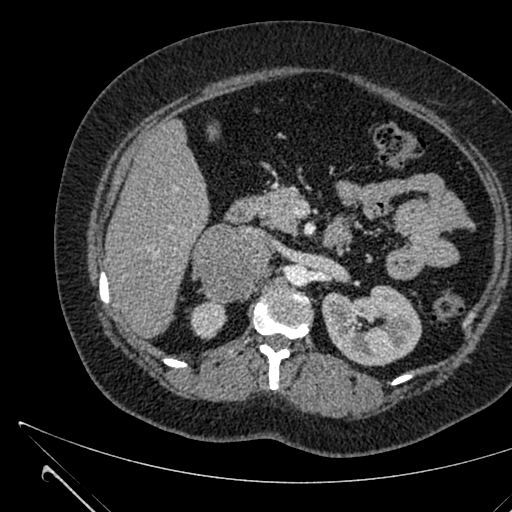
Contrast-enhanced abdominal CT, one axial slice; slice 383 of 731 in the series (ordered by position); soft-tissue window (W 400 / L 40 HU); 1 mm slice thickness; 512 × 512 image matrix, field of view 376 × 376 mm. Patient: female, 36 years. From the clinical record (not read from this slice): diagnosis: adrenocortical carcinoma; tumour side: right adrenal; tumour size at pathology: 10 cm.
Structures marked on this image (semi-automatic segmentation, software-assisted and operator-edited):
- mass: bounding box [x1, y1, x2, y2] px = [194, 225, 270, 302]